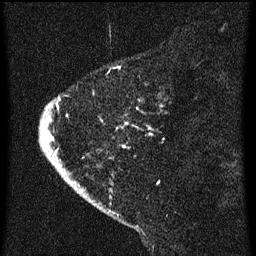
Breast MRI (dynamic contrast-enhanced), one sagittal slice; position 13 of 60 along the scan axis; dynamic contrast-enhanced series, image 2 of 3 at this slice position (ordered by acquisition); 1.5 T; TE 4.2 ms, TR 8 ms; 256 × 256 image matrix, field of view 180 × 180 mm. Female patient, age 47 years.
Annotated regions visible in this slice (semi-automatic segmentation, software-assisted and operator-edited):
- analysis volume of interest (the breast-tissue region the enhancement analysis was run in; not a lesion): bounding box (x1, y1, x2, y2) in pixels: (38, 76, 167, 193)
- tumour enhancement mask (voxels above the 70 % enhancement threshold inside the analysis volume of interest): (46, 98, 162, 167)